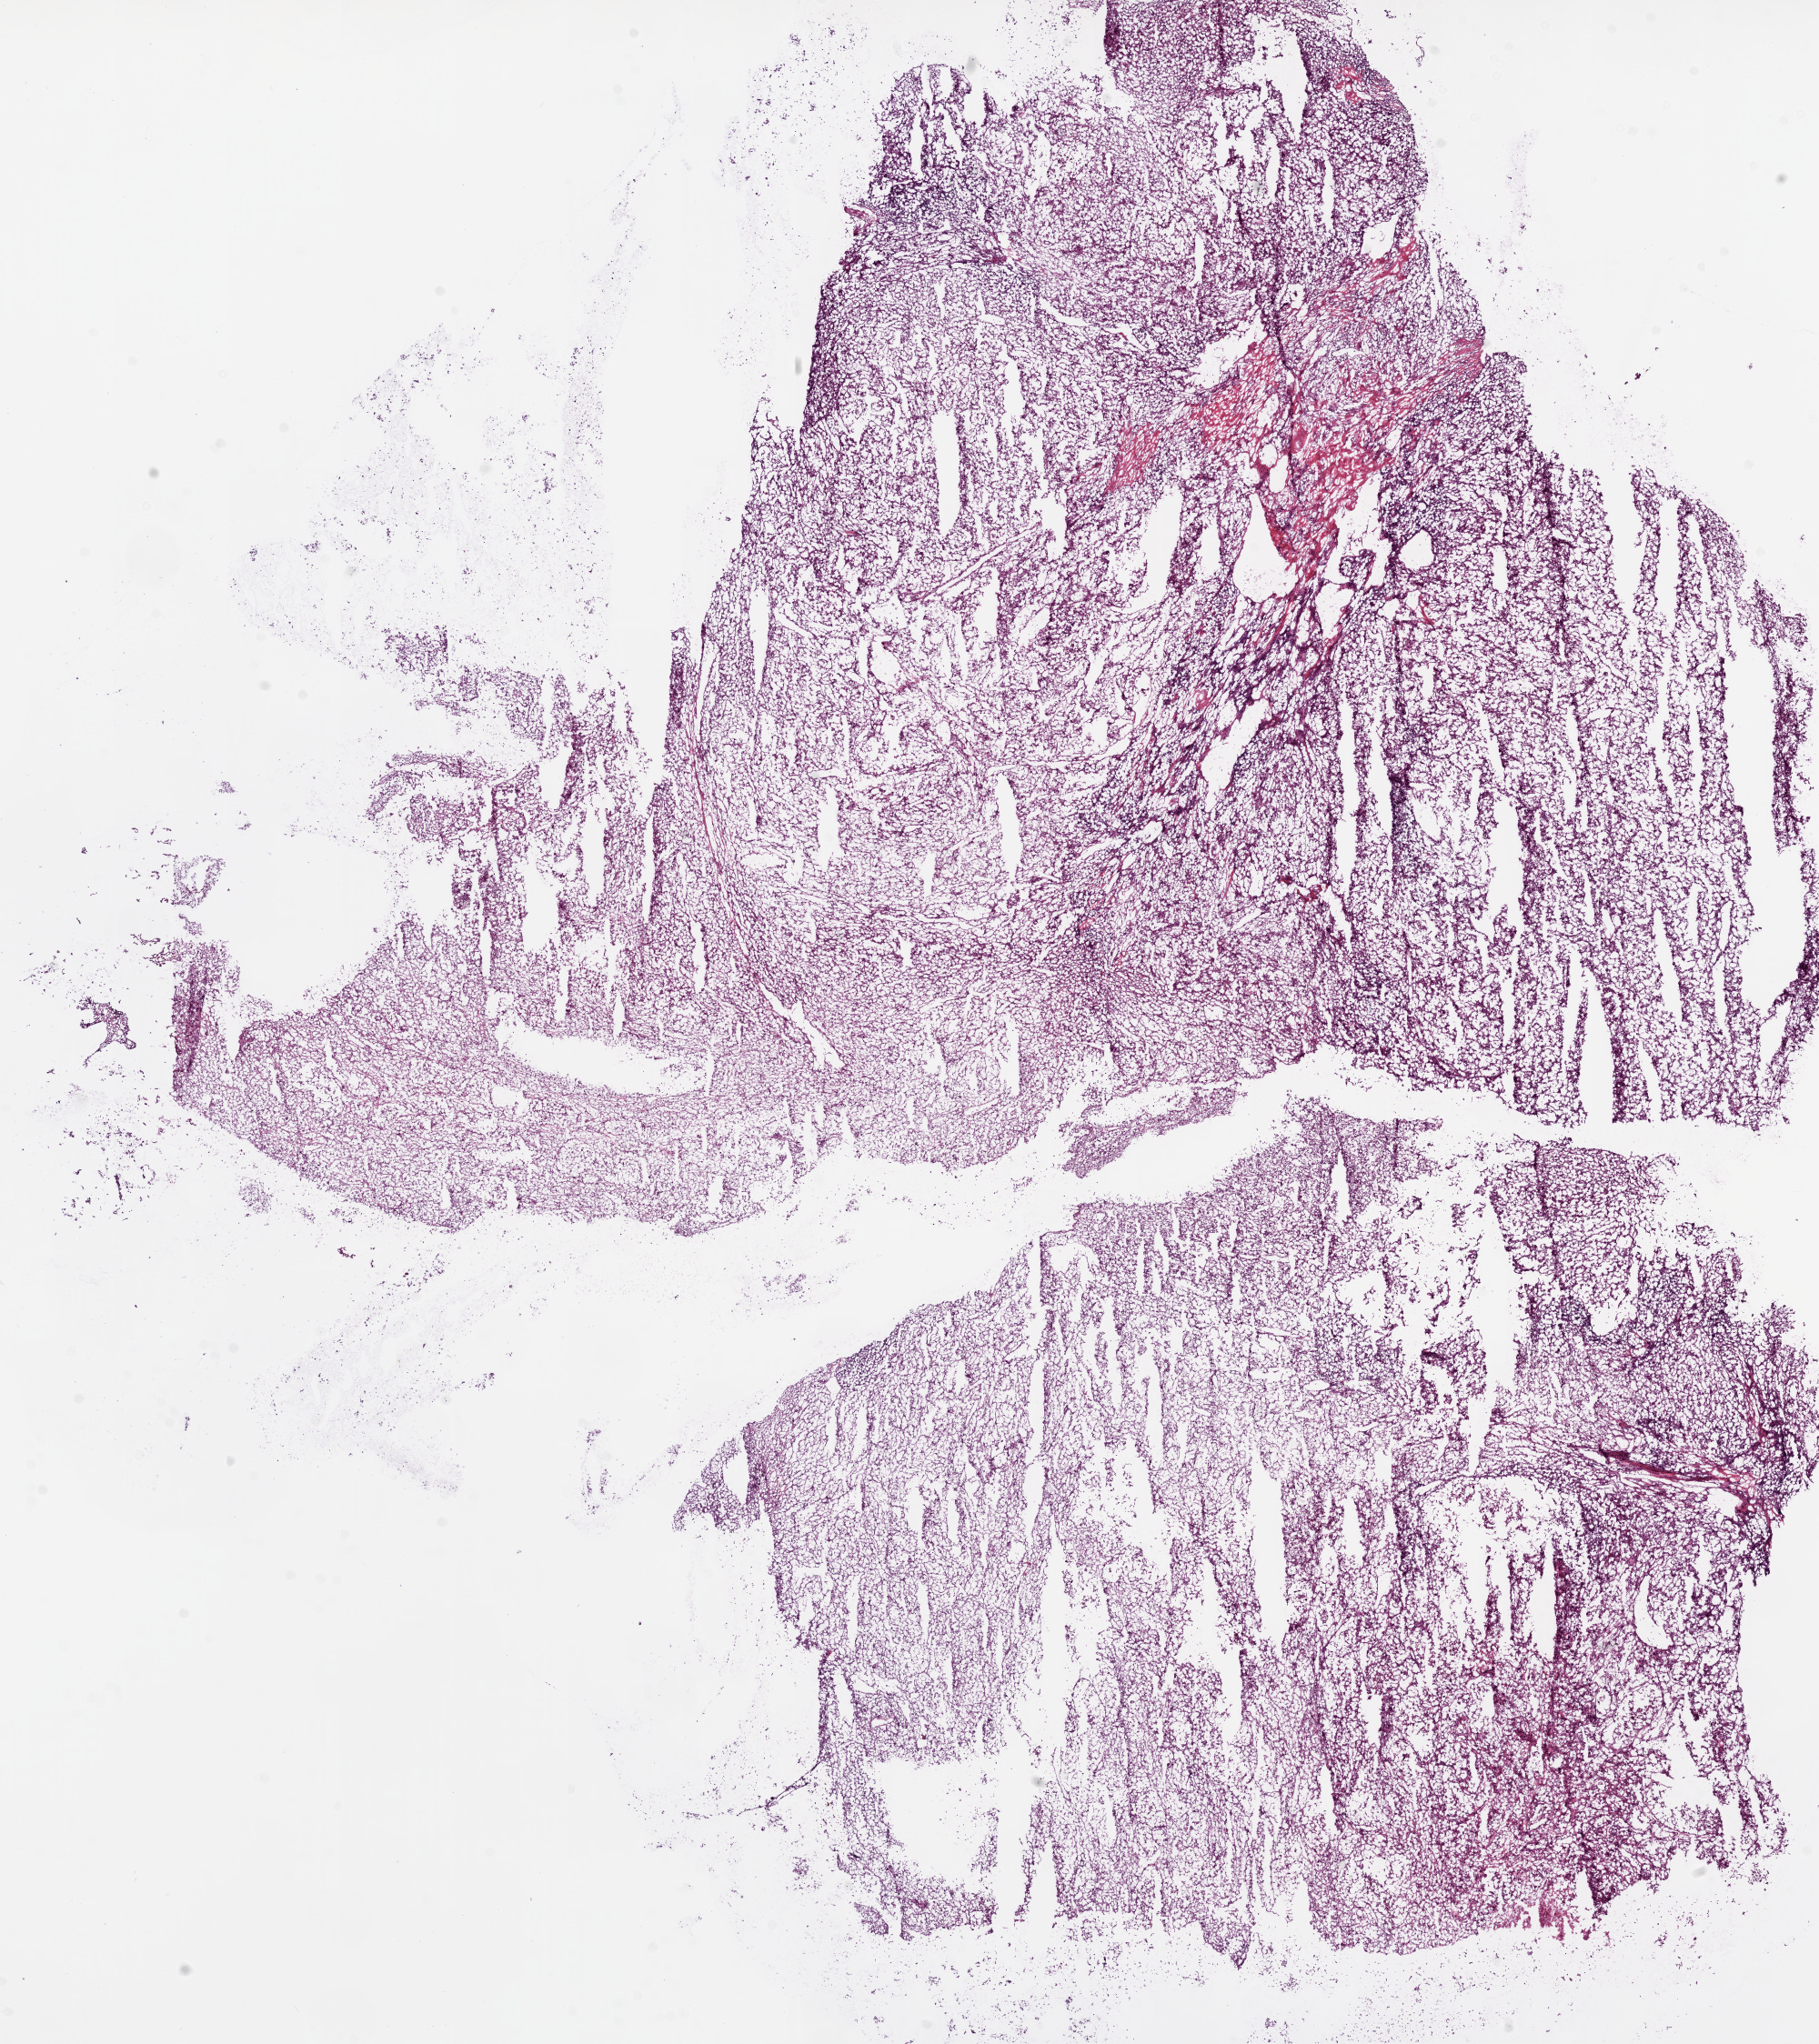
Hematoxylin and eosin (H&E) stained whole-slide image, shown as a low-resolution overview of the whole scanned area (about 16.0 x 18.0 mm). Frozen section. Kidney, primary tumour sample. Patient: female, age at initial diagnosis 73 years. Pathologist review of this section (percent, as recorded): tumour cells 95%, tumour nuclei 90%.
Pathologic diagnosis: Clear cell adenocarcinoma, NOS.